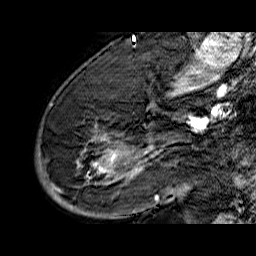
Breast MRI (dynamic contrast-enhanced), one sagittal slice. Position 42 of 60 along the scan axis. Dynamic contrast-enhanced series, time point 2 of 6 at this slice position (early post-contrast). 1.5 T. TE 6.5 ms, TR 32.9 ms. 4 mm slice thickness. 256 × 256 image matrix, field of view 200 × 200 mm. Female patient. Case-level facts recorded for this patient, not image findings: setting: breast cancer imaged before/during neoadjuvant chemotherapy; receptor status: HR-positive, HER2-negative.
Outlined on this slice (semi-automatic segmentation, software-assisted and operator-edited):
- analysis volume of interest (the breast-tissue region the enhancement analysis was run in; not a lesion): box from (x=36, y=74) to (x=176, y=210) px
- tumour enhancement mask (voxels above the 100 % enhancement threshold inside the analysis volume of interest): (x=50, y=105)–(x=161, y=201)